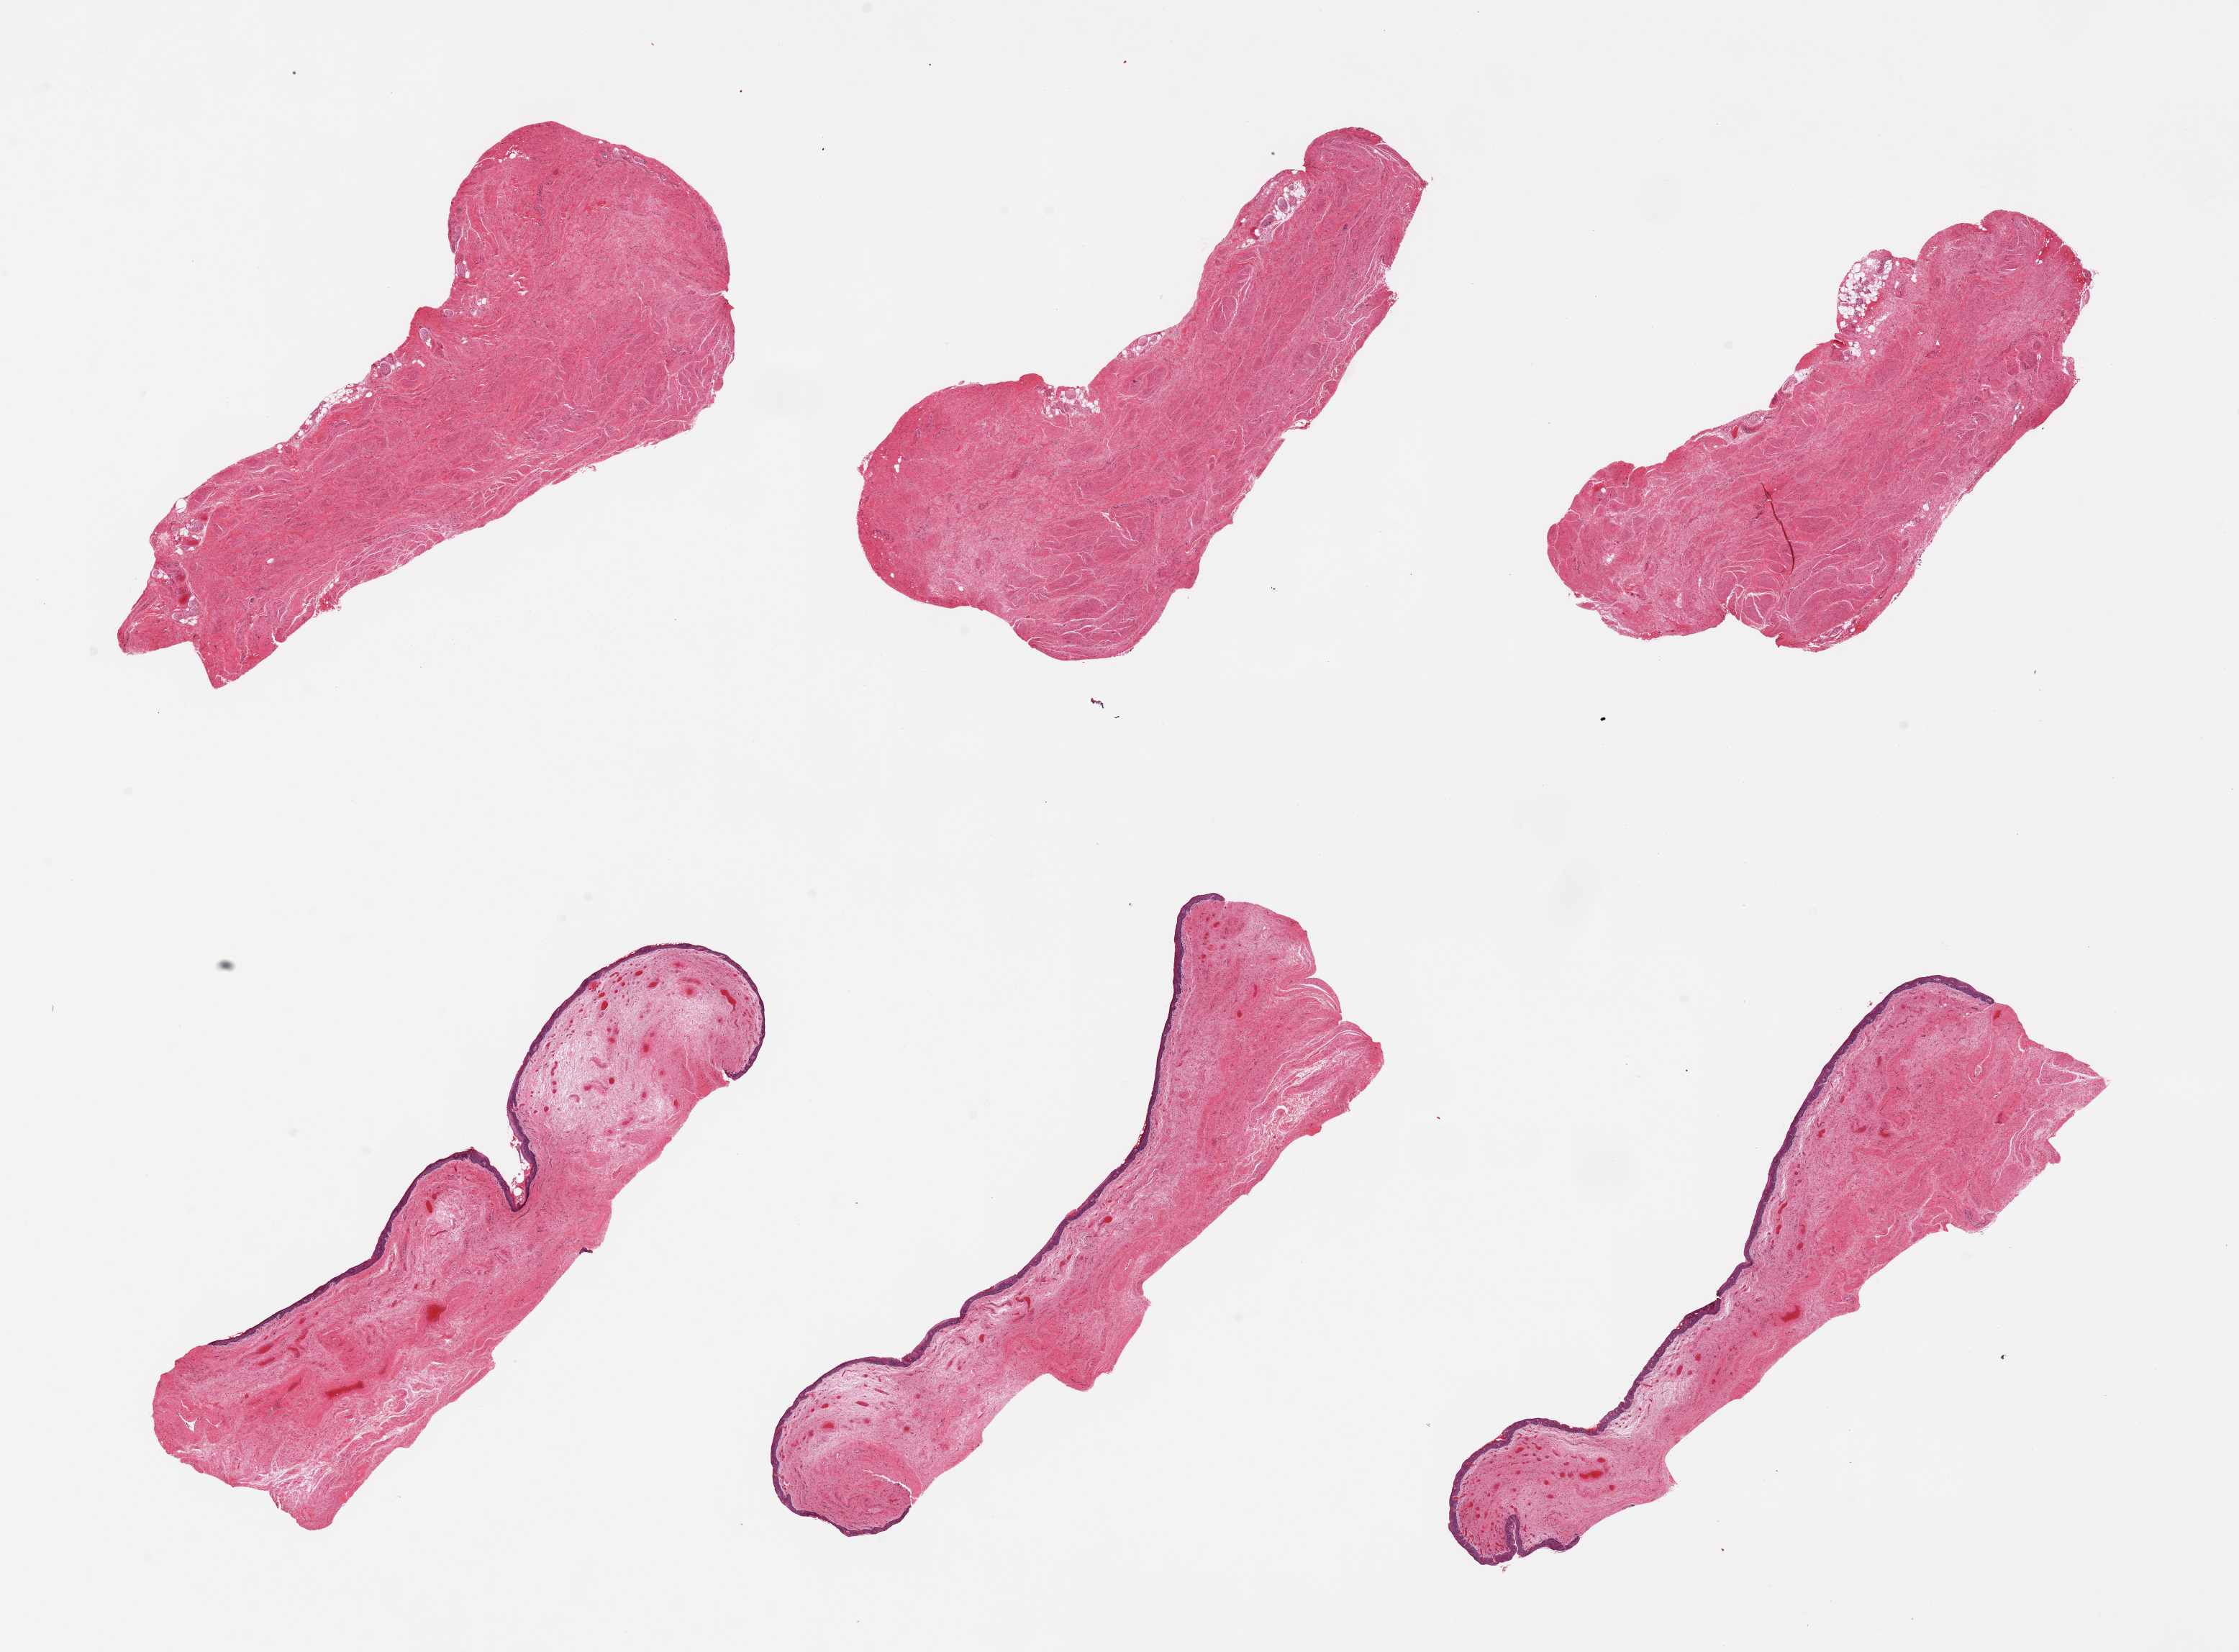
Digitized haematoxylin and eosin-stained section, a low-resolution overview of the entire scanned area, about 24.6 x 18.2 mm (from a 20x scan); PAXgene-fixed paraffin-embedded (PFPE) section; sampled site (target tissue): vagina; donor tissue sample. Donor: female.
Reviewer comment on this tissue sample: 6 pieces, squamous mucosa visible on 3, ~5% thickness.